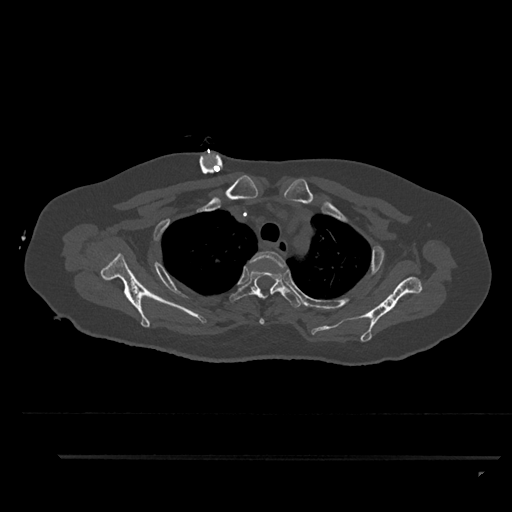
CT including the spine, one axial slice; slice 696 of 797 in the series (ordered by position); 120 kVp; bone window (W 1800 / L 400 HU); 0.5 mm slice thickness; 512 × 512 image matrix, field of view 408 × 408 mm. Female patient, age 44 years. Case-level facts recorded for this patient, not image findings: primary cancer: renal.
Annotated regions visible in this slice (semi-automatically segmented with operator editing):
- T2 vertebra: box from (x=249, y=251) to (x=287, y=325) px
- T3 vertebra: (x=229, y=268)–(x=304, y=308)